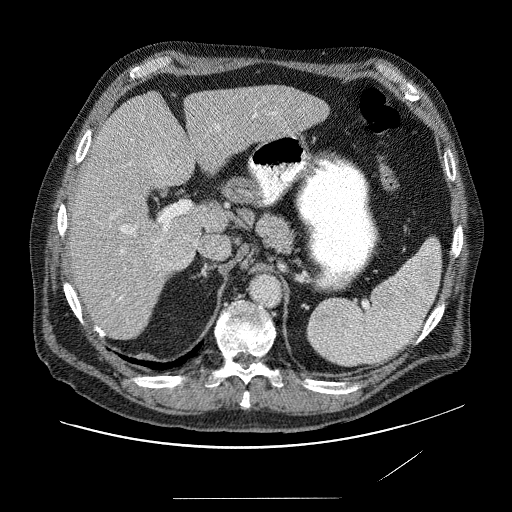
Contrast-enhanced abdominal CT (liver protocol), one axial slice. Slice 47 of 89 in the series (ordered by position). Reconstruction kernel STANDARD. Soft-tissue window (W 400 / L 40 HU). 2.5 mm slice thickness. 512 × 512 image matrix. Case-level facts recorded for this patient, not image findings: diagnosis: hepatocellular carcinoma (patient treated with transarterial chemoembolisation; whether this scan precedes or follows treatment is not stated here); TNM stage (as recorded): Stage-IVA; Child-Pugh class: A; tumour nodularity: multinodular.
Annotated regions visible in this slice (semi-automatically segmented with operator editing):
- abdominal aorta: bounding box <250,275,280,305> (left, top, right, bottom; pixels)
- liver parenchyma outside the tumour (the mass and vessels are separate outlines, so this box may not span the whole liver): <62,84,332,336>
- mass: <146,138,195,262>
- liver vessels: <103,116,280,315>